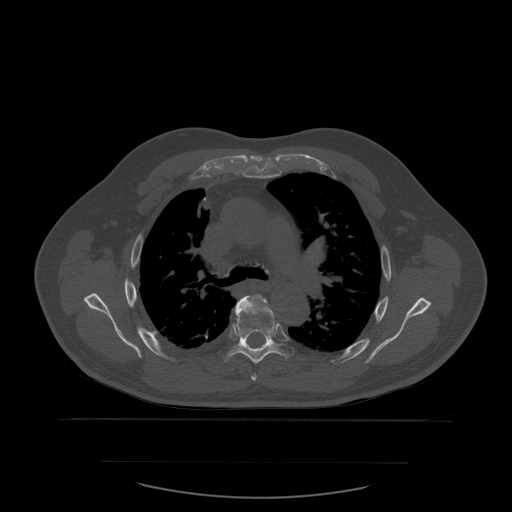
CT including the spine, one axial slice. Position 408 of 590 along the scan axis. Bone window (W 1800 / L 400 HU). 1.25 mm slice thickness. 512 × 512 image matrix, field of view 479 × 479 mm. Patient age 71 years. From the clinical record (not read from this slice): primary cancer: lung; vertebrae with lytic lesions (as recorded): T1, T2, L5, S1.
Annotated regions visible in this slice (semi-automatic segmentation, software-assisted and operator-edited):
- T5 vertebra: bounding box <237,295,273,381> (left, top, right, bottom; pixels)
- T6 vertebra: <218,296,294,365>